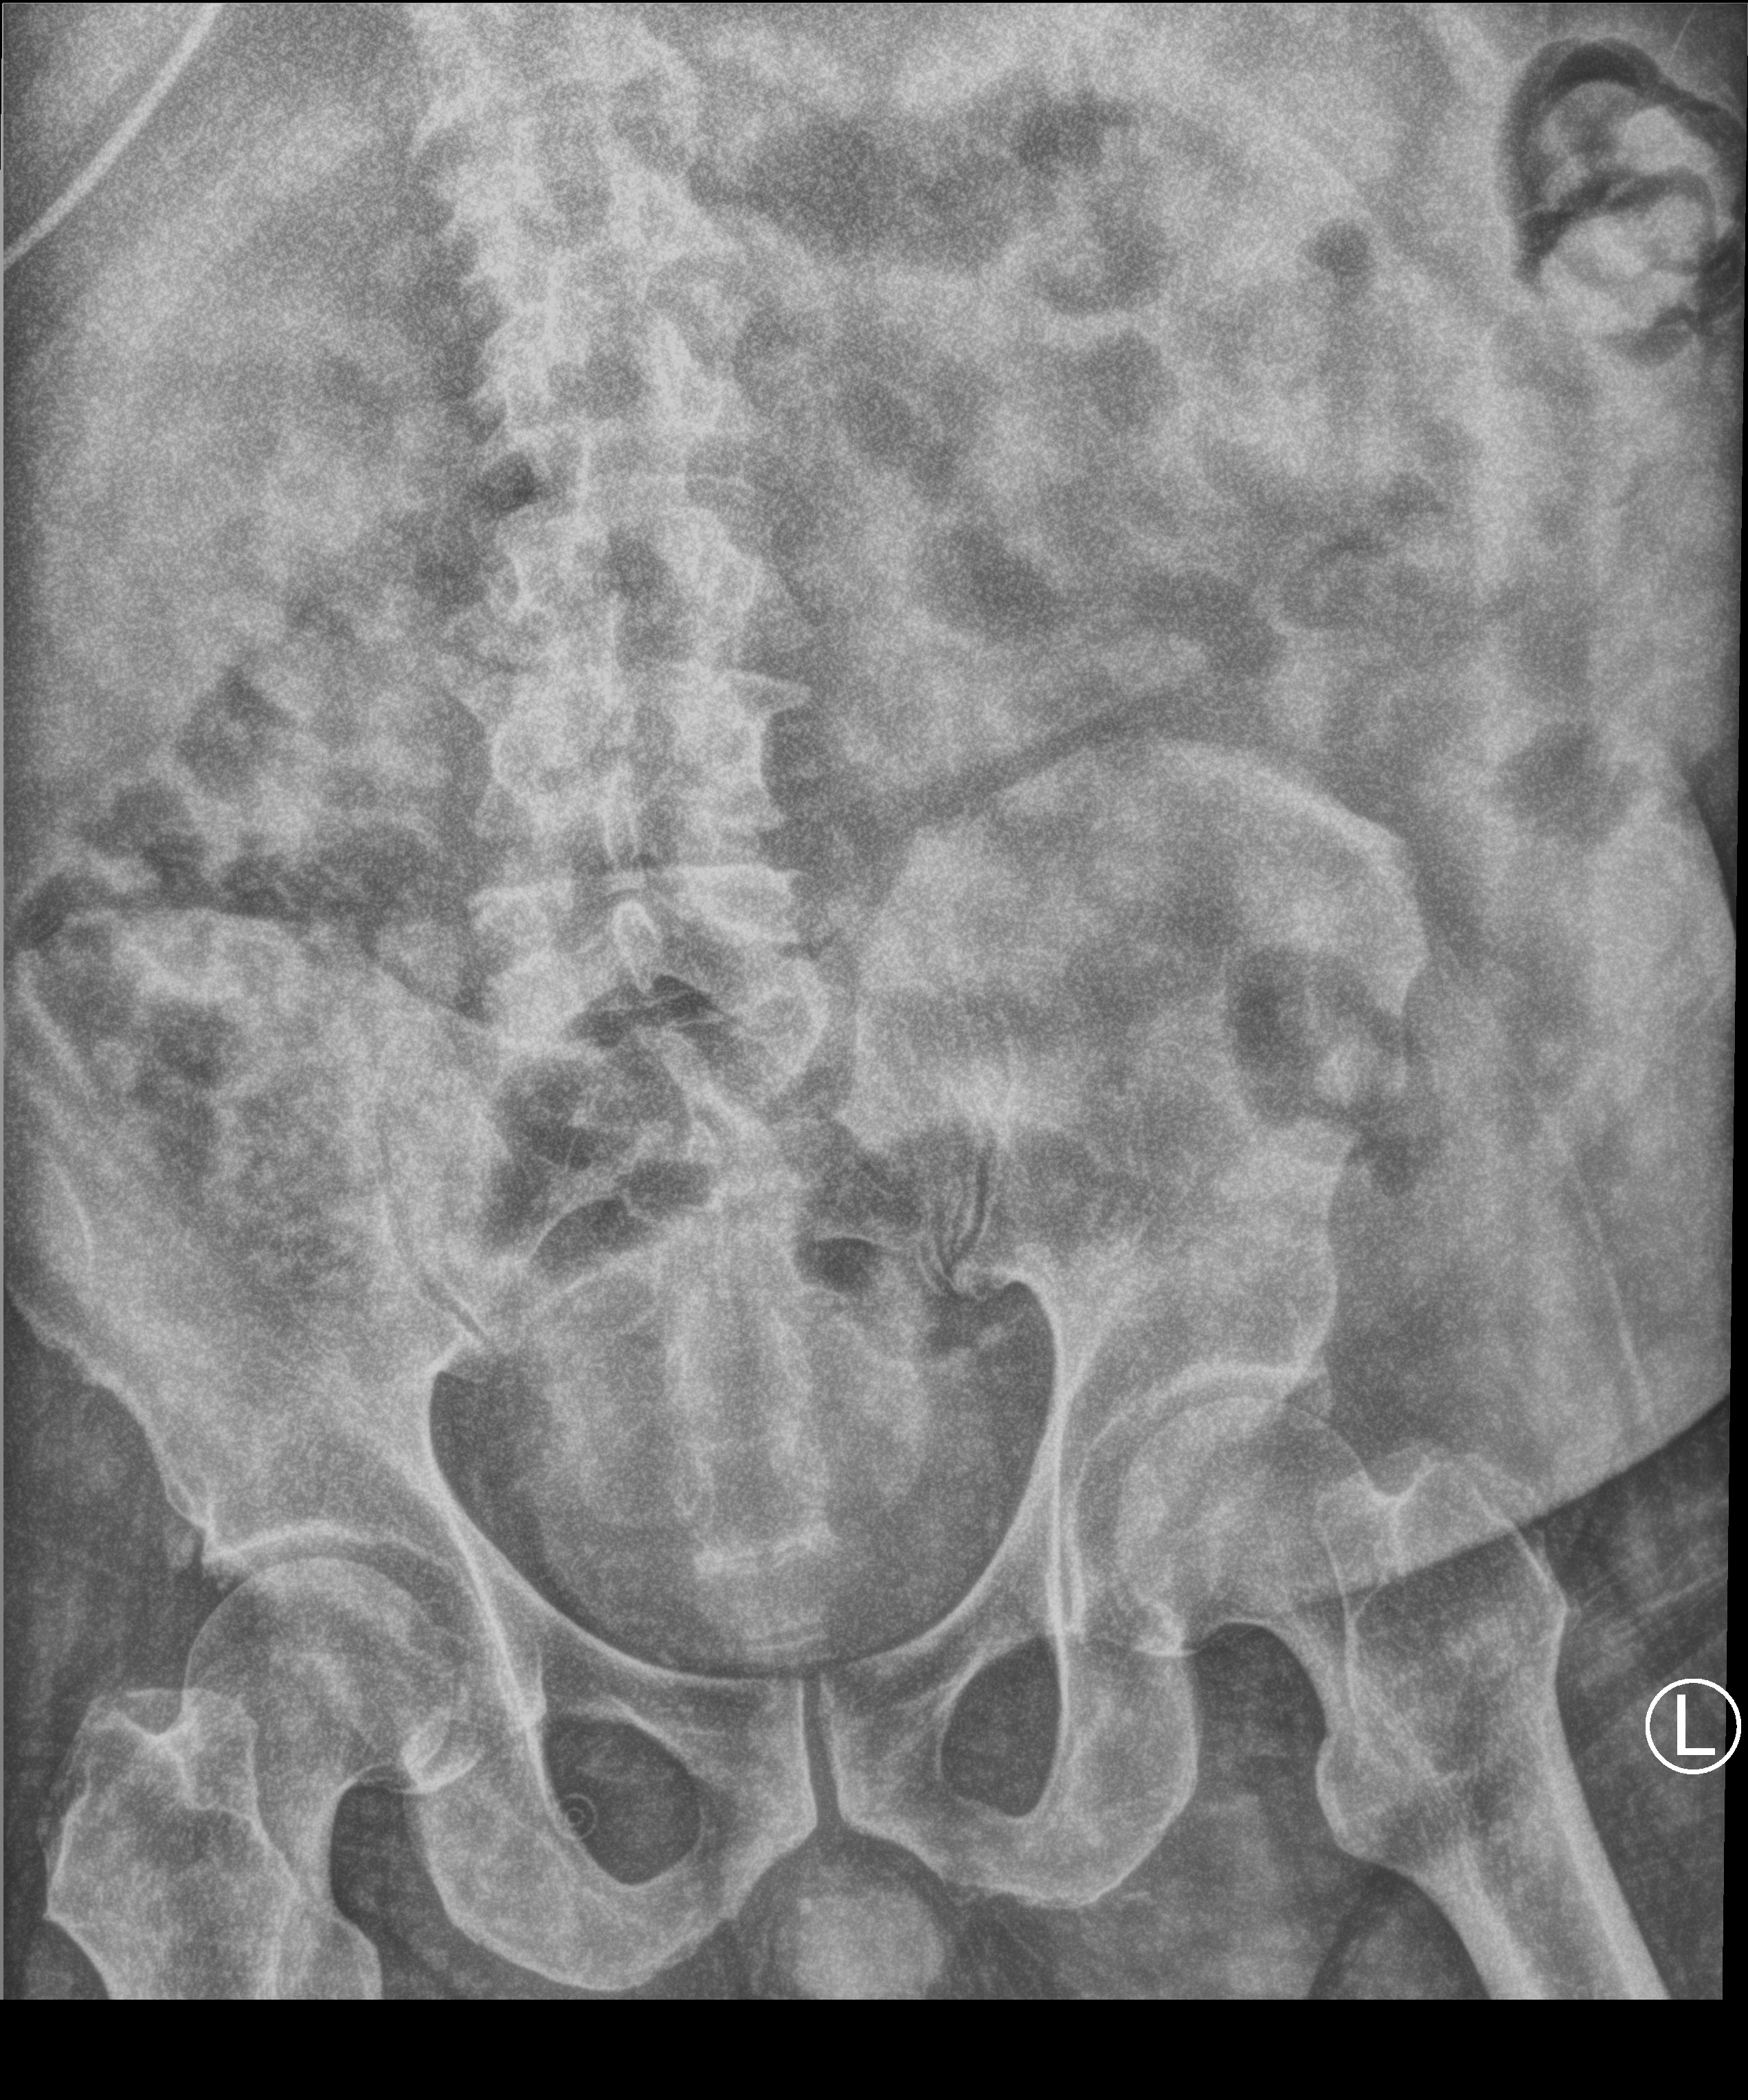
Portable abdomen radiograph, anteroposterior (AP) projection. Male patient hospitalised with COVID-19, age 18–59 years.
From the hospital-stay record, not from the radiograph (when in the stay this image was taken is not recorded): admitted to intensive care during this hospital stay: no; length of hospital stay: 18 days; mechanically ventilated during this hospital stay: no.